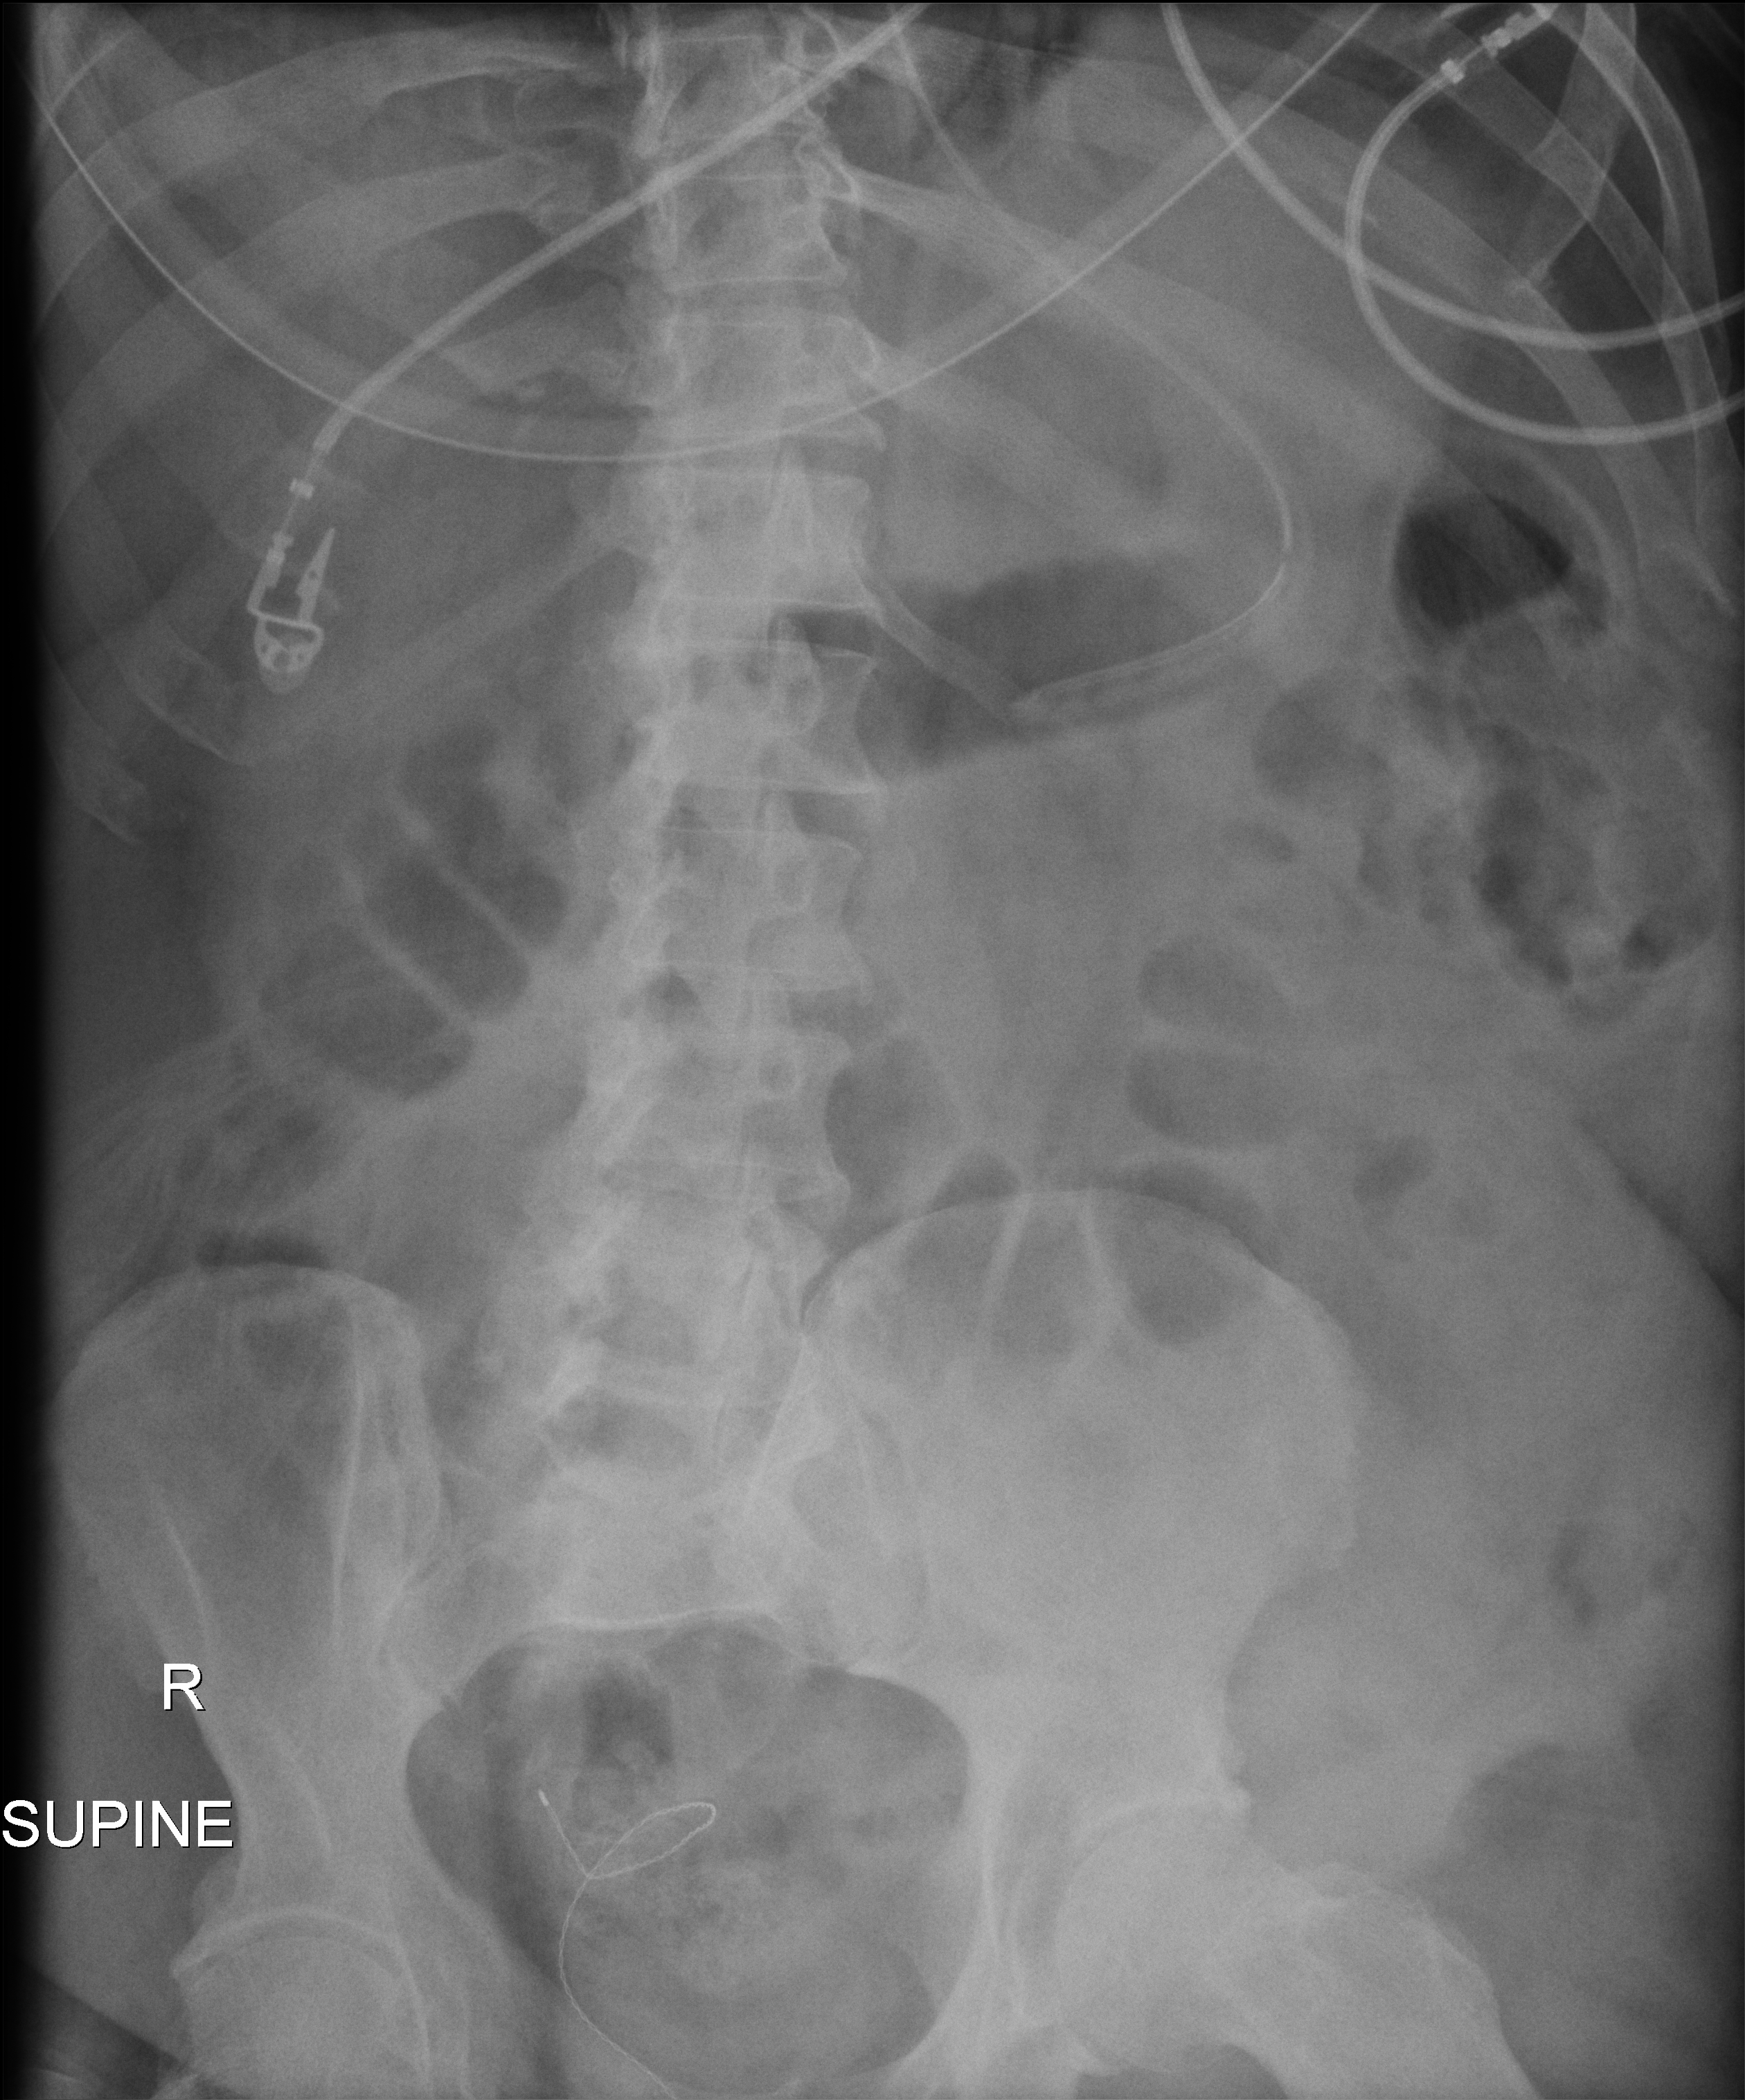
Portable abdomen radiograph; anteroposterior (AP) projection. Male patient hospitalised with COVID-19, age 18–59 years.
Admission-level facts for this patient (not findings on this image; timing relative to this image not recorded):
- admitted to intensive care during this hospital stay: yes